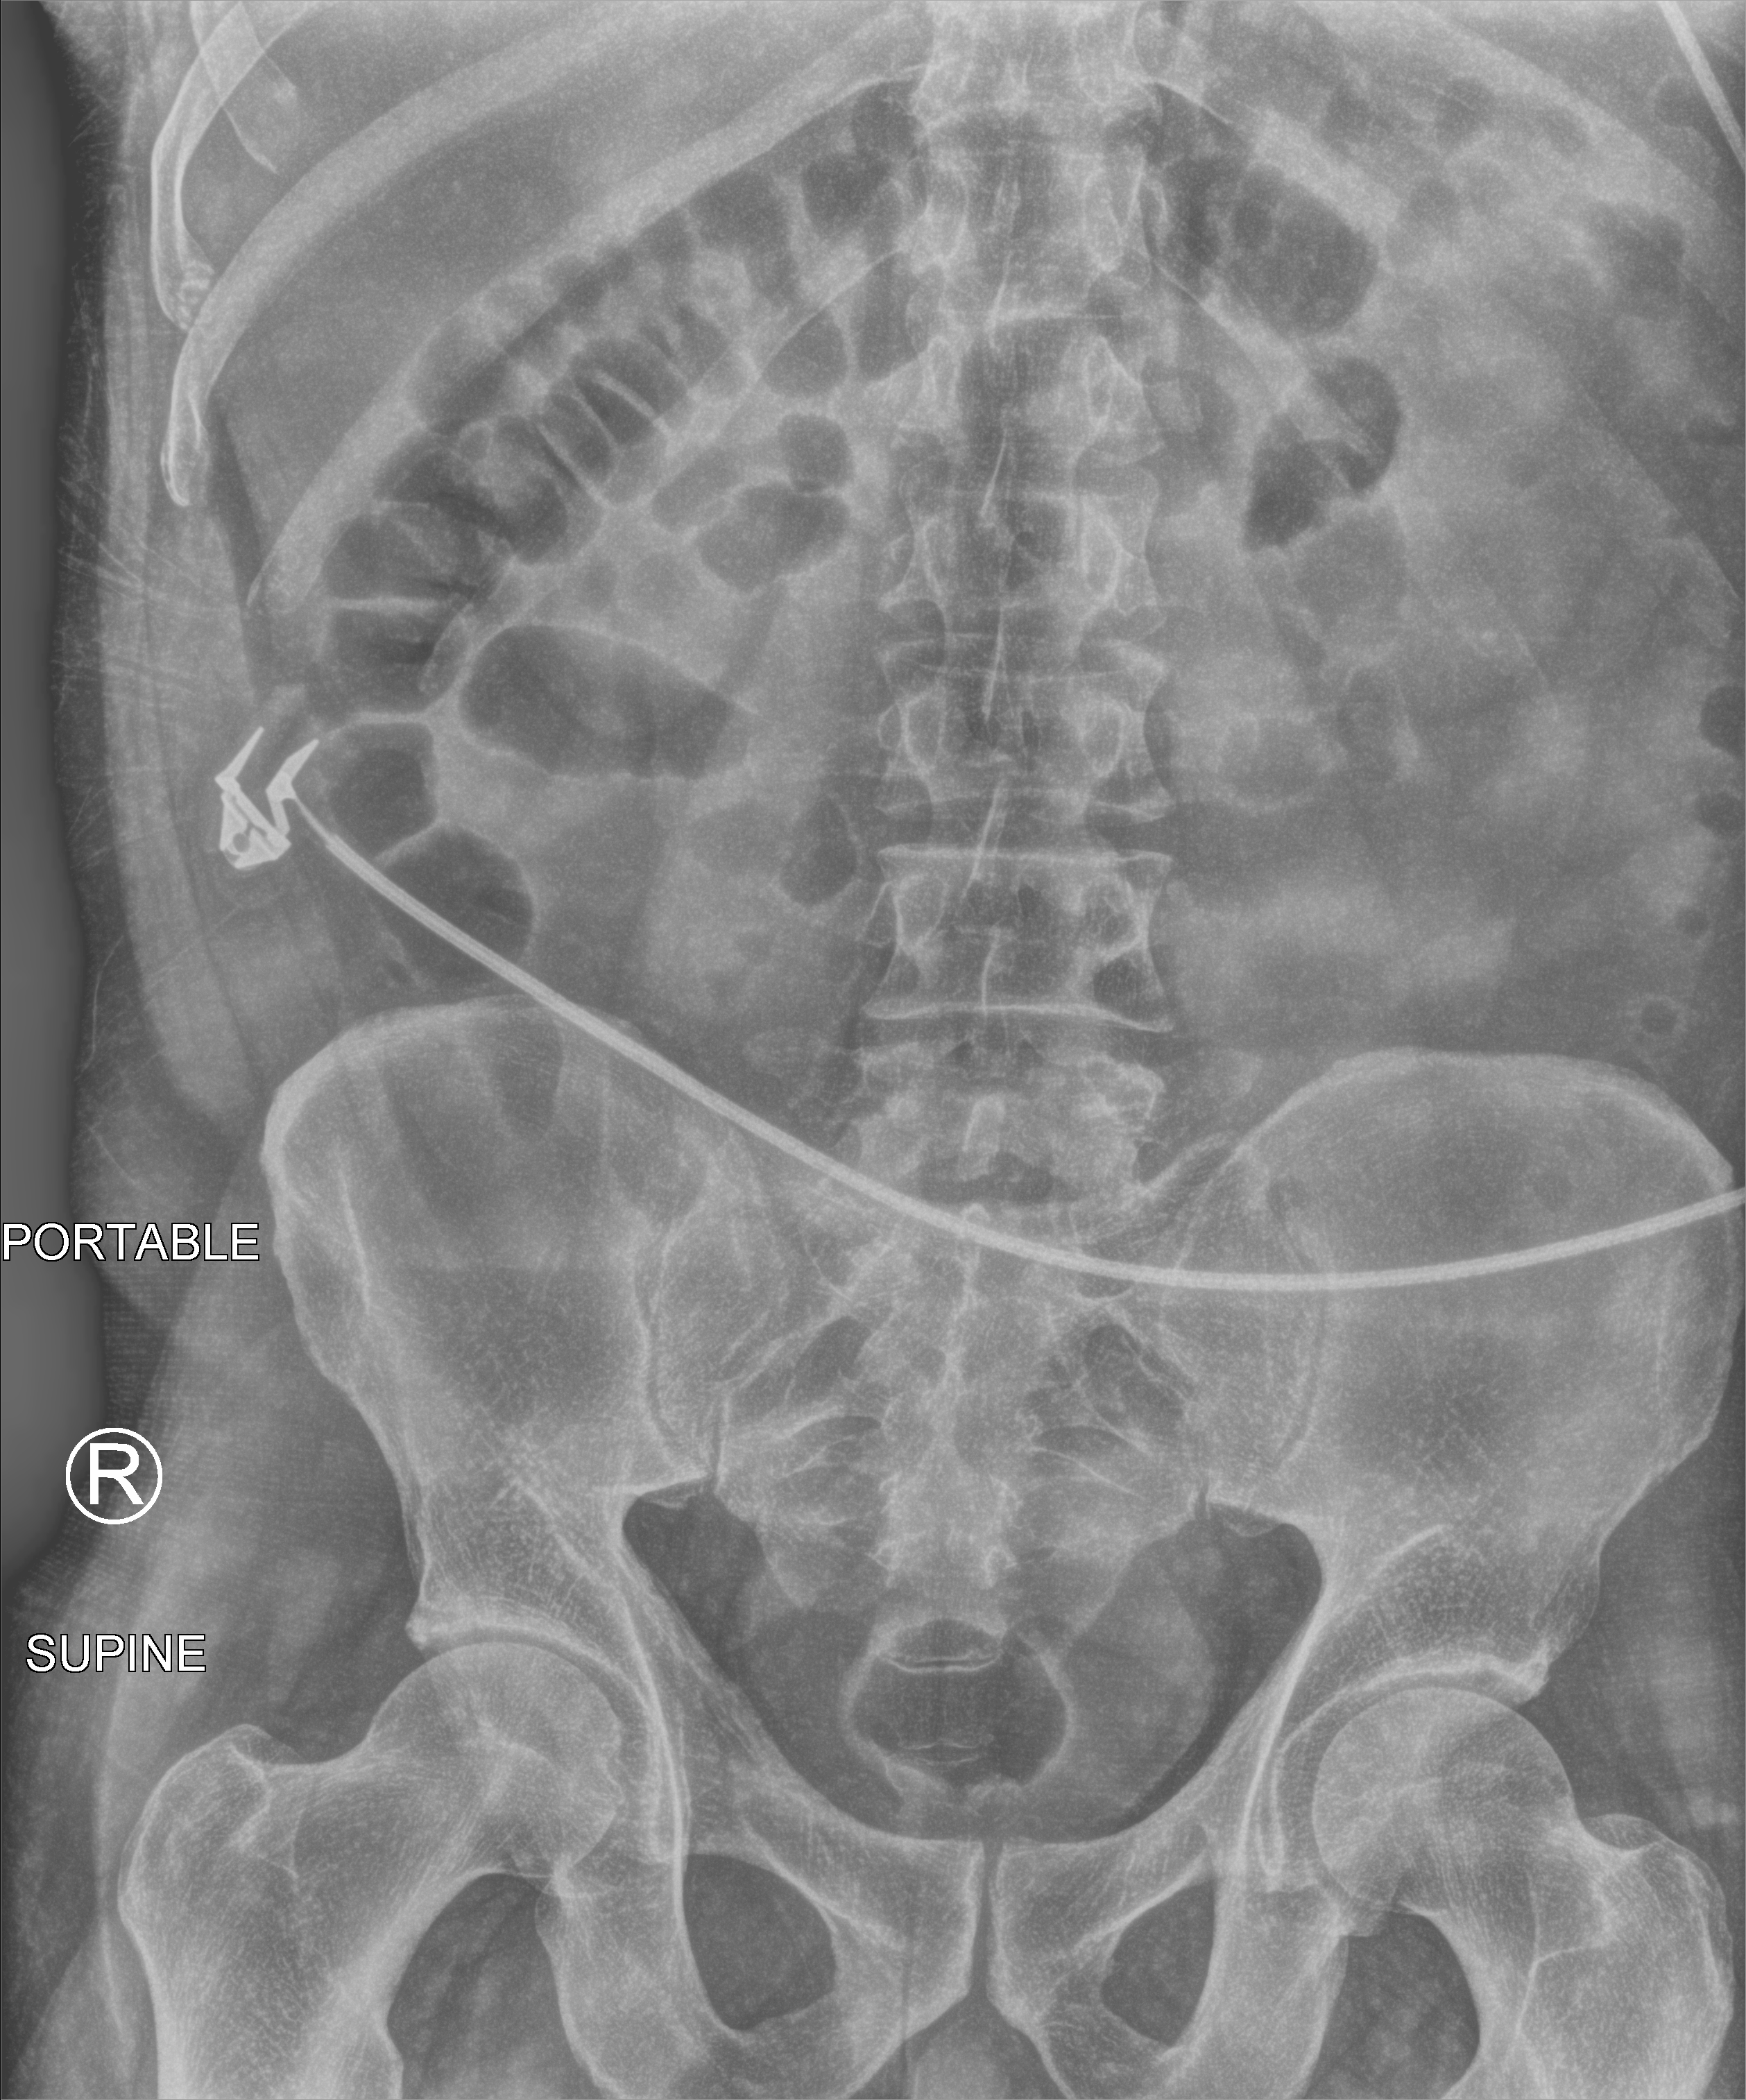
Portable abdomen radiograph. Patient hospitalised with COVID-19; male, aged 18–59 years.
Admission-level facts for this patient (not findings on this image; timing relative to this image not recorded): admitted to intensive care during this hospital stay: no; diabetes (admission record): no; length of hospital stay: 4 days.